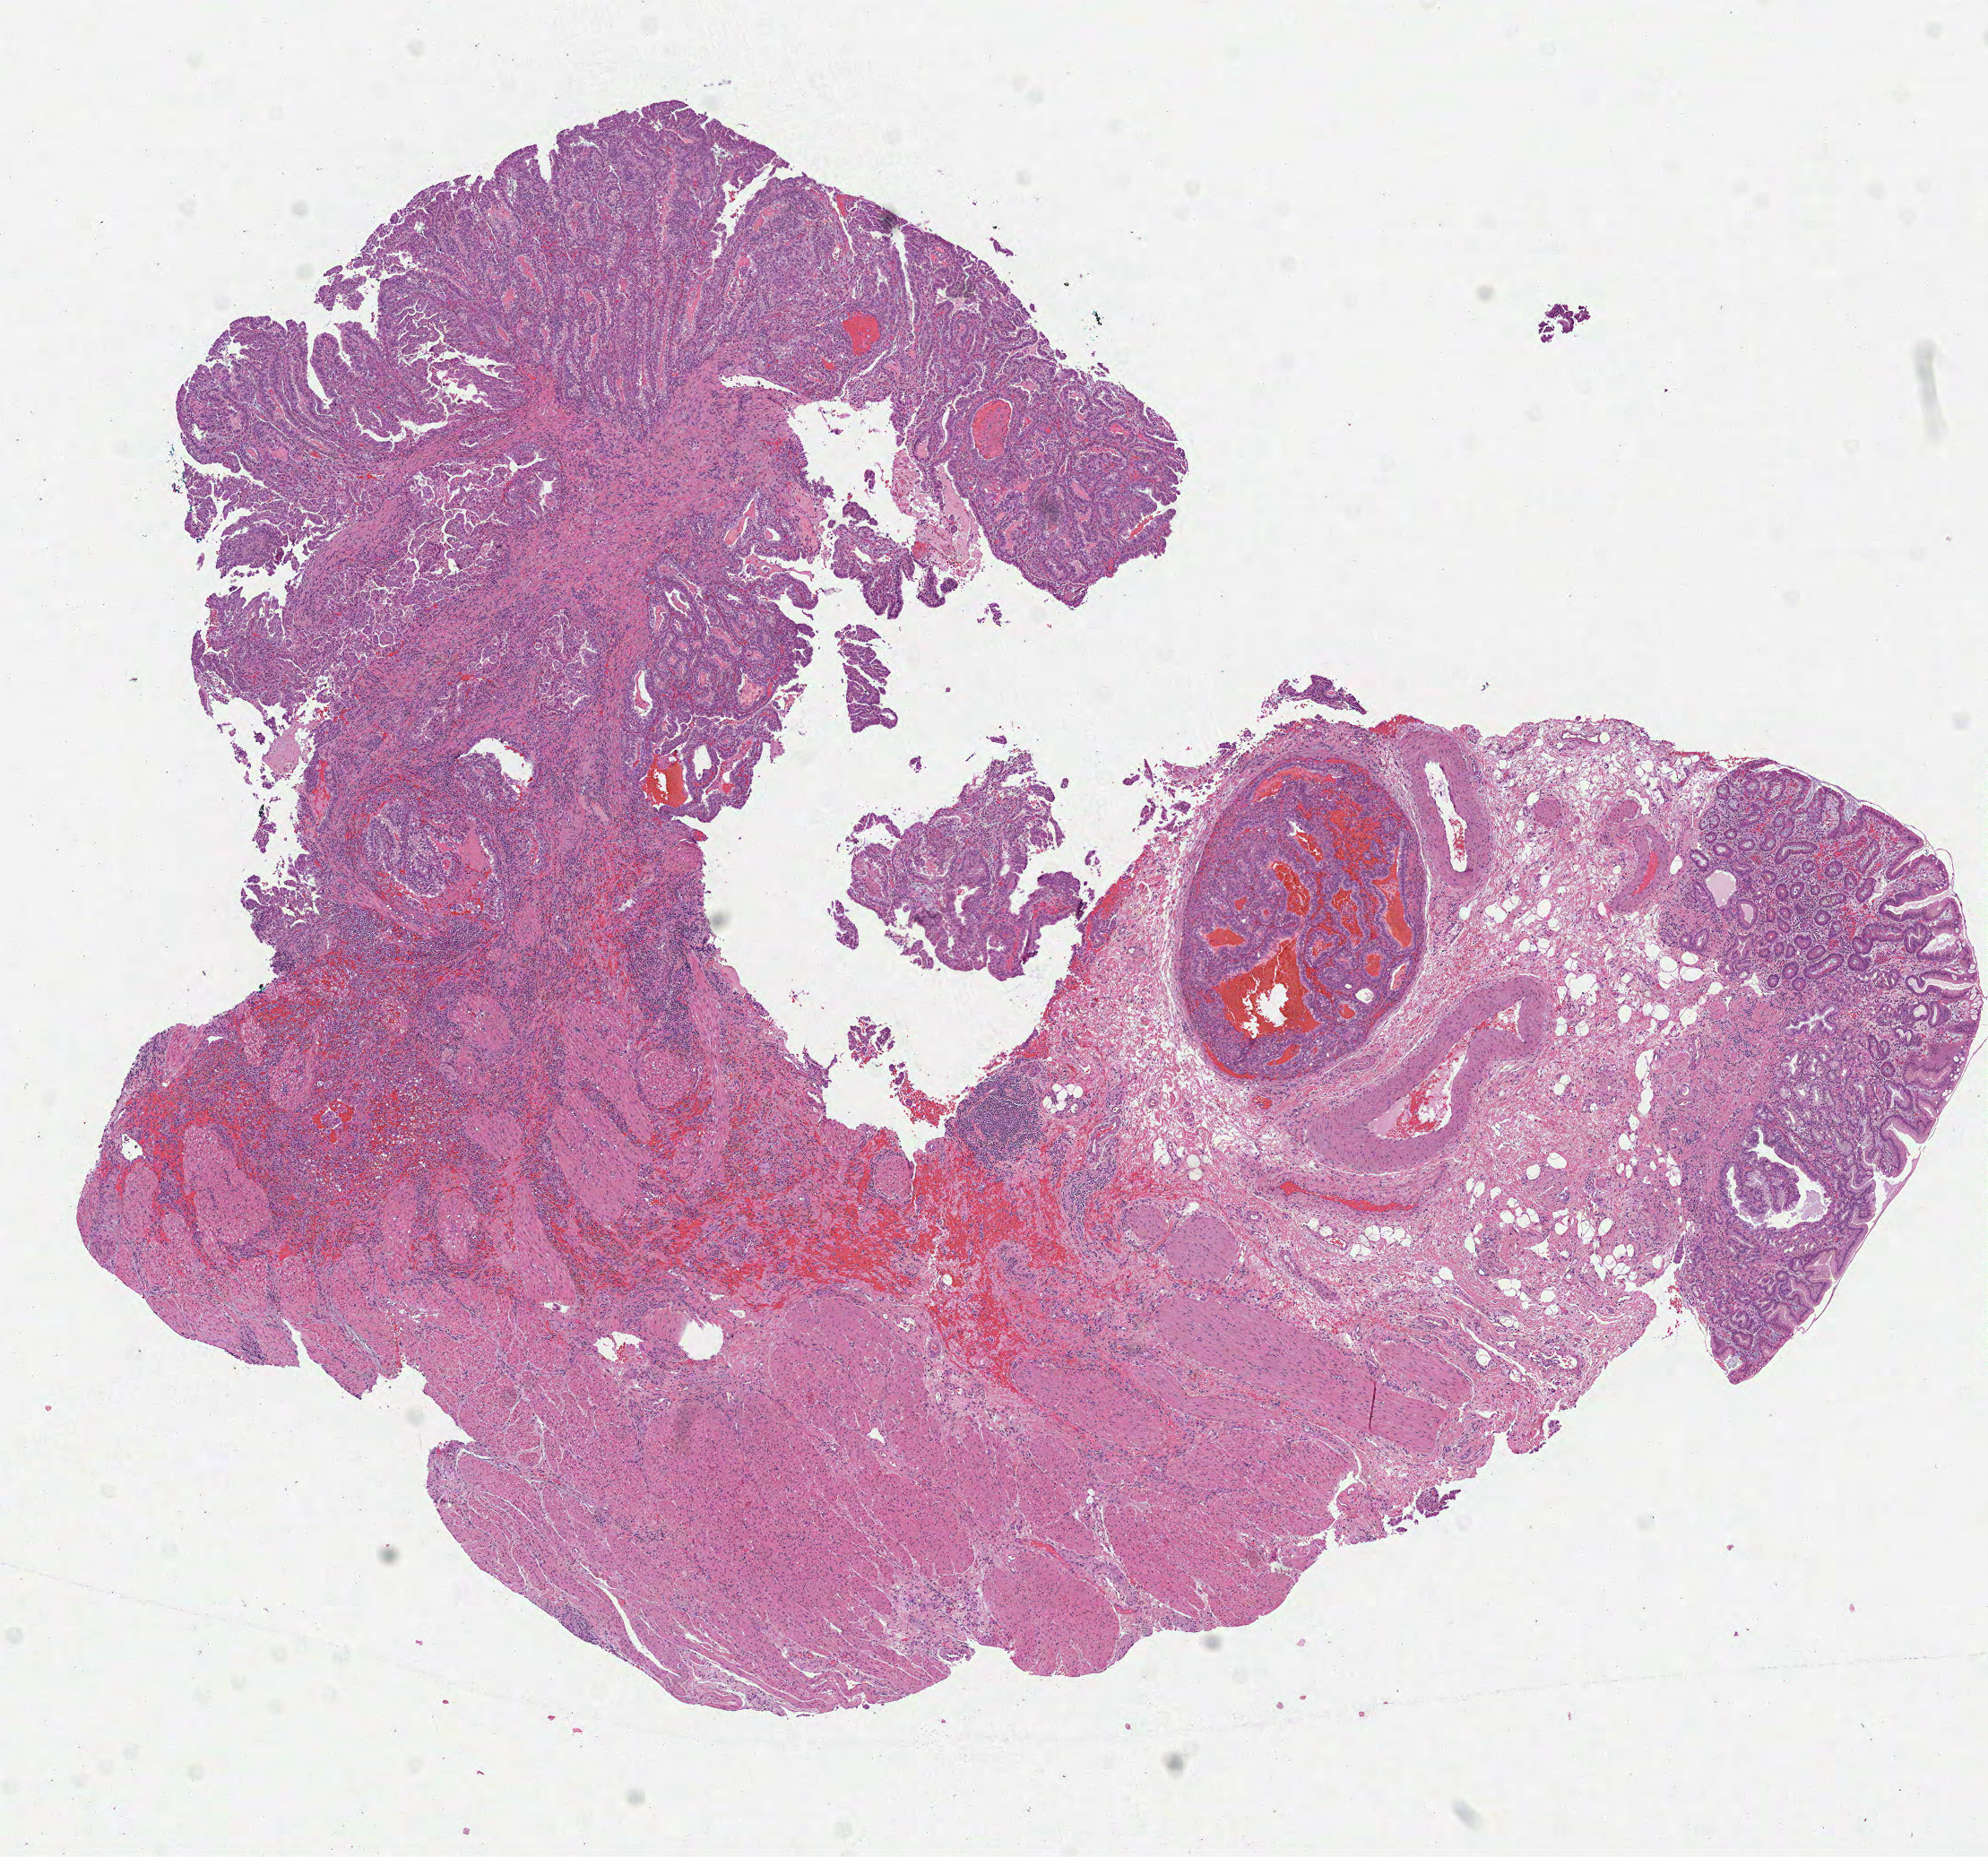
Hematoxylin and eosin (H&E) stained whole-slide image — shown as a low-resolution overview of the whole scanned area (about 8.9 x 8.4 mm, acquisition: 40x scan), formalin-fixed paraffin-embedded (FFPE) diagnostic section, primary tumour sample from the stomach. Male patient; age at initial diagnosis 77 years.
Histologic diagnosis: Adenocarcinoma, NOS (cardia, NOS).